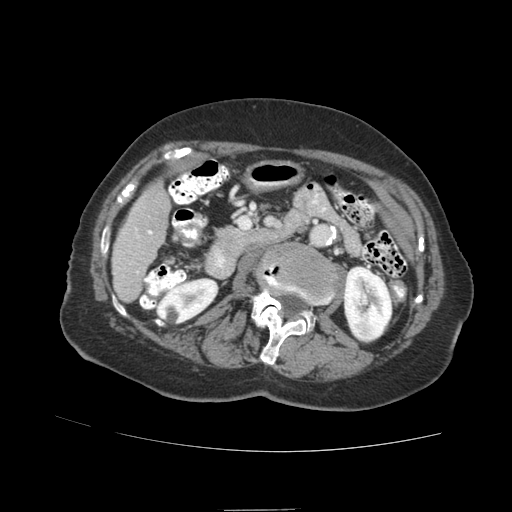
Contrast-enhanced abdominal CT (liver protocol), one axial slice; position 24 of 89 along the scan axis; reconstruction kernel STANDARD; 140 kVp; soft-tissue window (W 400 / L 40 HU); 512 × 512 image matrix, field of view 360 × 360 mm. From the clinical record (not read from this slice): diagnosis: hepatocellular carcinoma (patient treated with transarterial chemoembolisation; whether this scan precedes or follows treatment is not stated here); TNM stage (as recorded): Stage-II; Child-Pugh class: A; tumour nodularity: multinodular; tumour size: 4 cm.
Structures marked on this image (semi-automatically segmented with operator editing):
- liver parenchyma outside the tumour (the mass and vessels are separate outlines, so this box may not span the whole liver): box from (x=112, y=182) to (x=170, y=302) px
- liver vessels: (x=136, y=229)–(x=152, y=274)